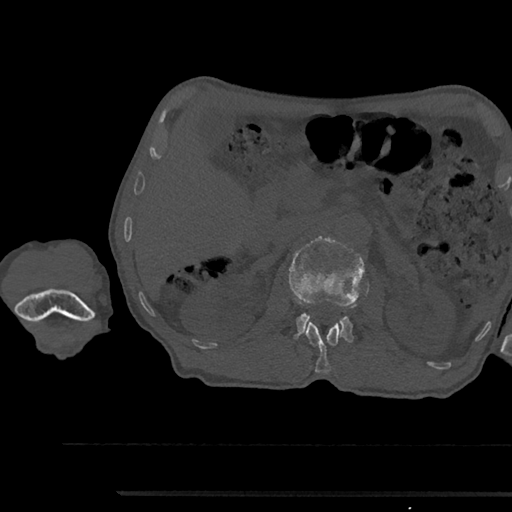
CT including the spine, one axial slice. Slice 603 of 797 in the series (ordered by position). Bone window (W 1800 / L 400 HU). 0.5 mm slice thickness. 512 × 512 image matrix. Male patient, age 79 years. Case-level facts recorded for this patient, not image findings: primary cancer: prostate.
Annotated regions visible in this slice (semi-automatic segmentation, software-assisted and operator-edited):
- L1 vertebra: bounding box [x1, y1, x2, y2] px = [305, 322, 341, 373]
- L2 vertebra: [289, 236, 366, 343]